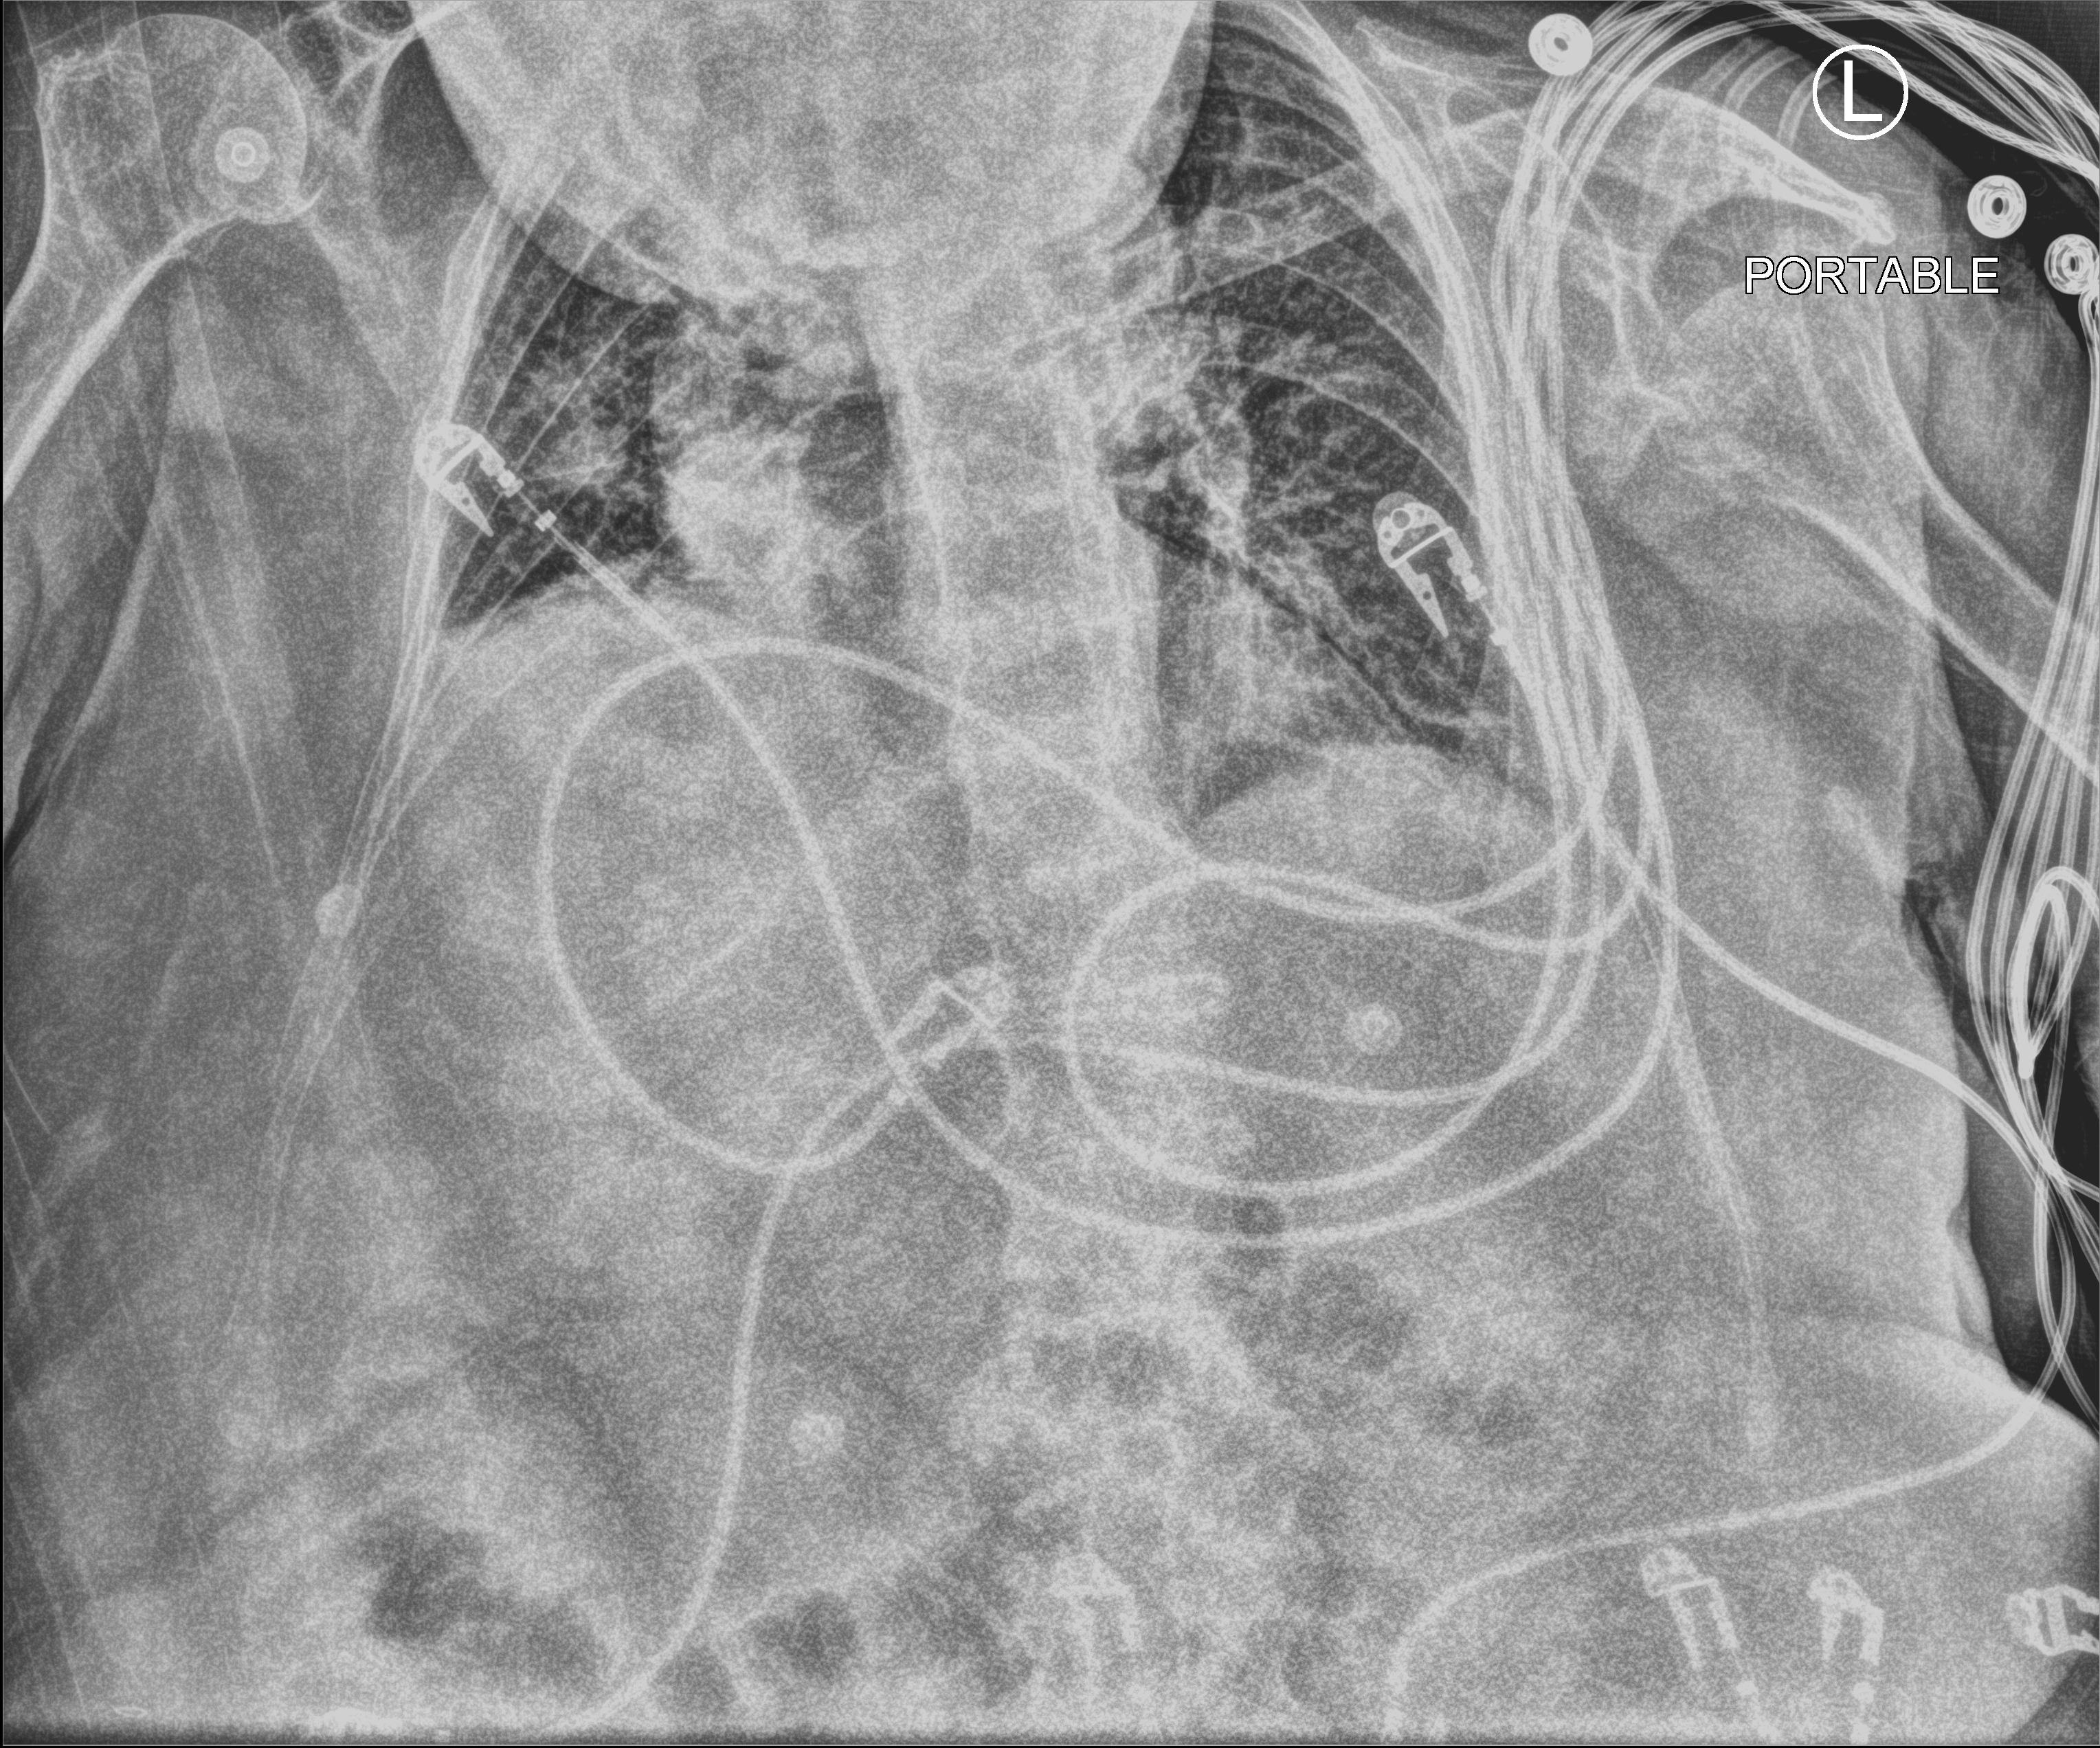
Chest X-ray (portable); anteroposterior (AP) projection. Patient hospitalised with COVID-19; female, aged 75–90 years.
Admission-level facts for this patient (not findings on this image; timing relative to this image not recorded): mechanically ventilated during this hospital stay: yes; admitted to intensive care during this hospital stay: yes.